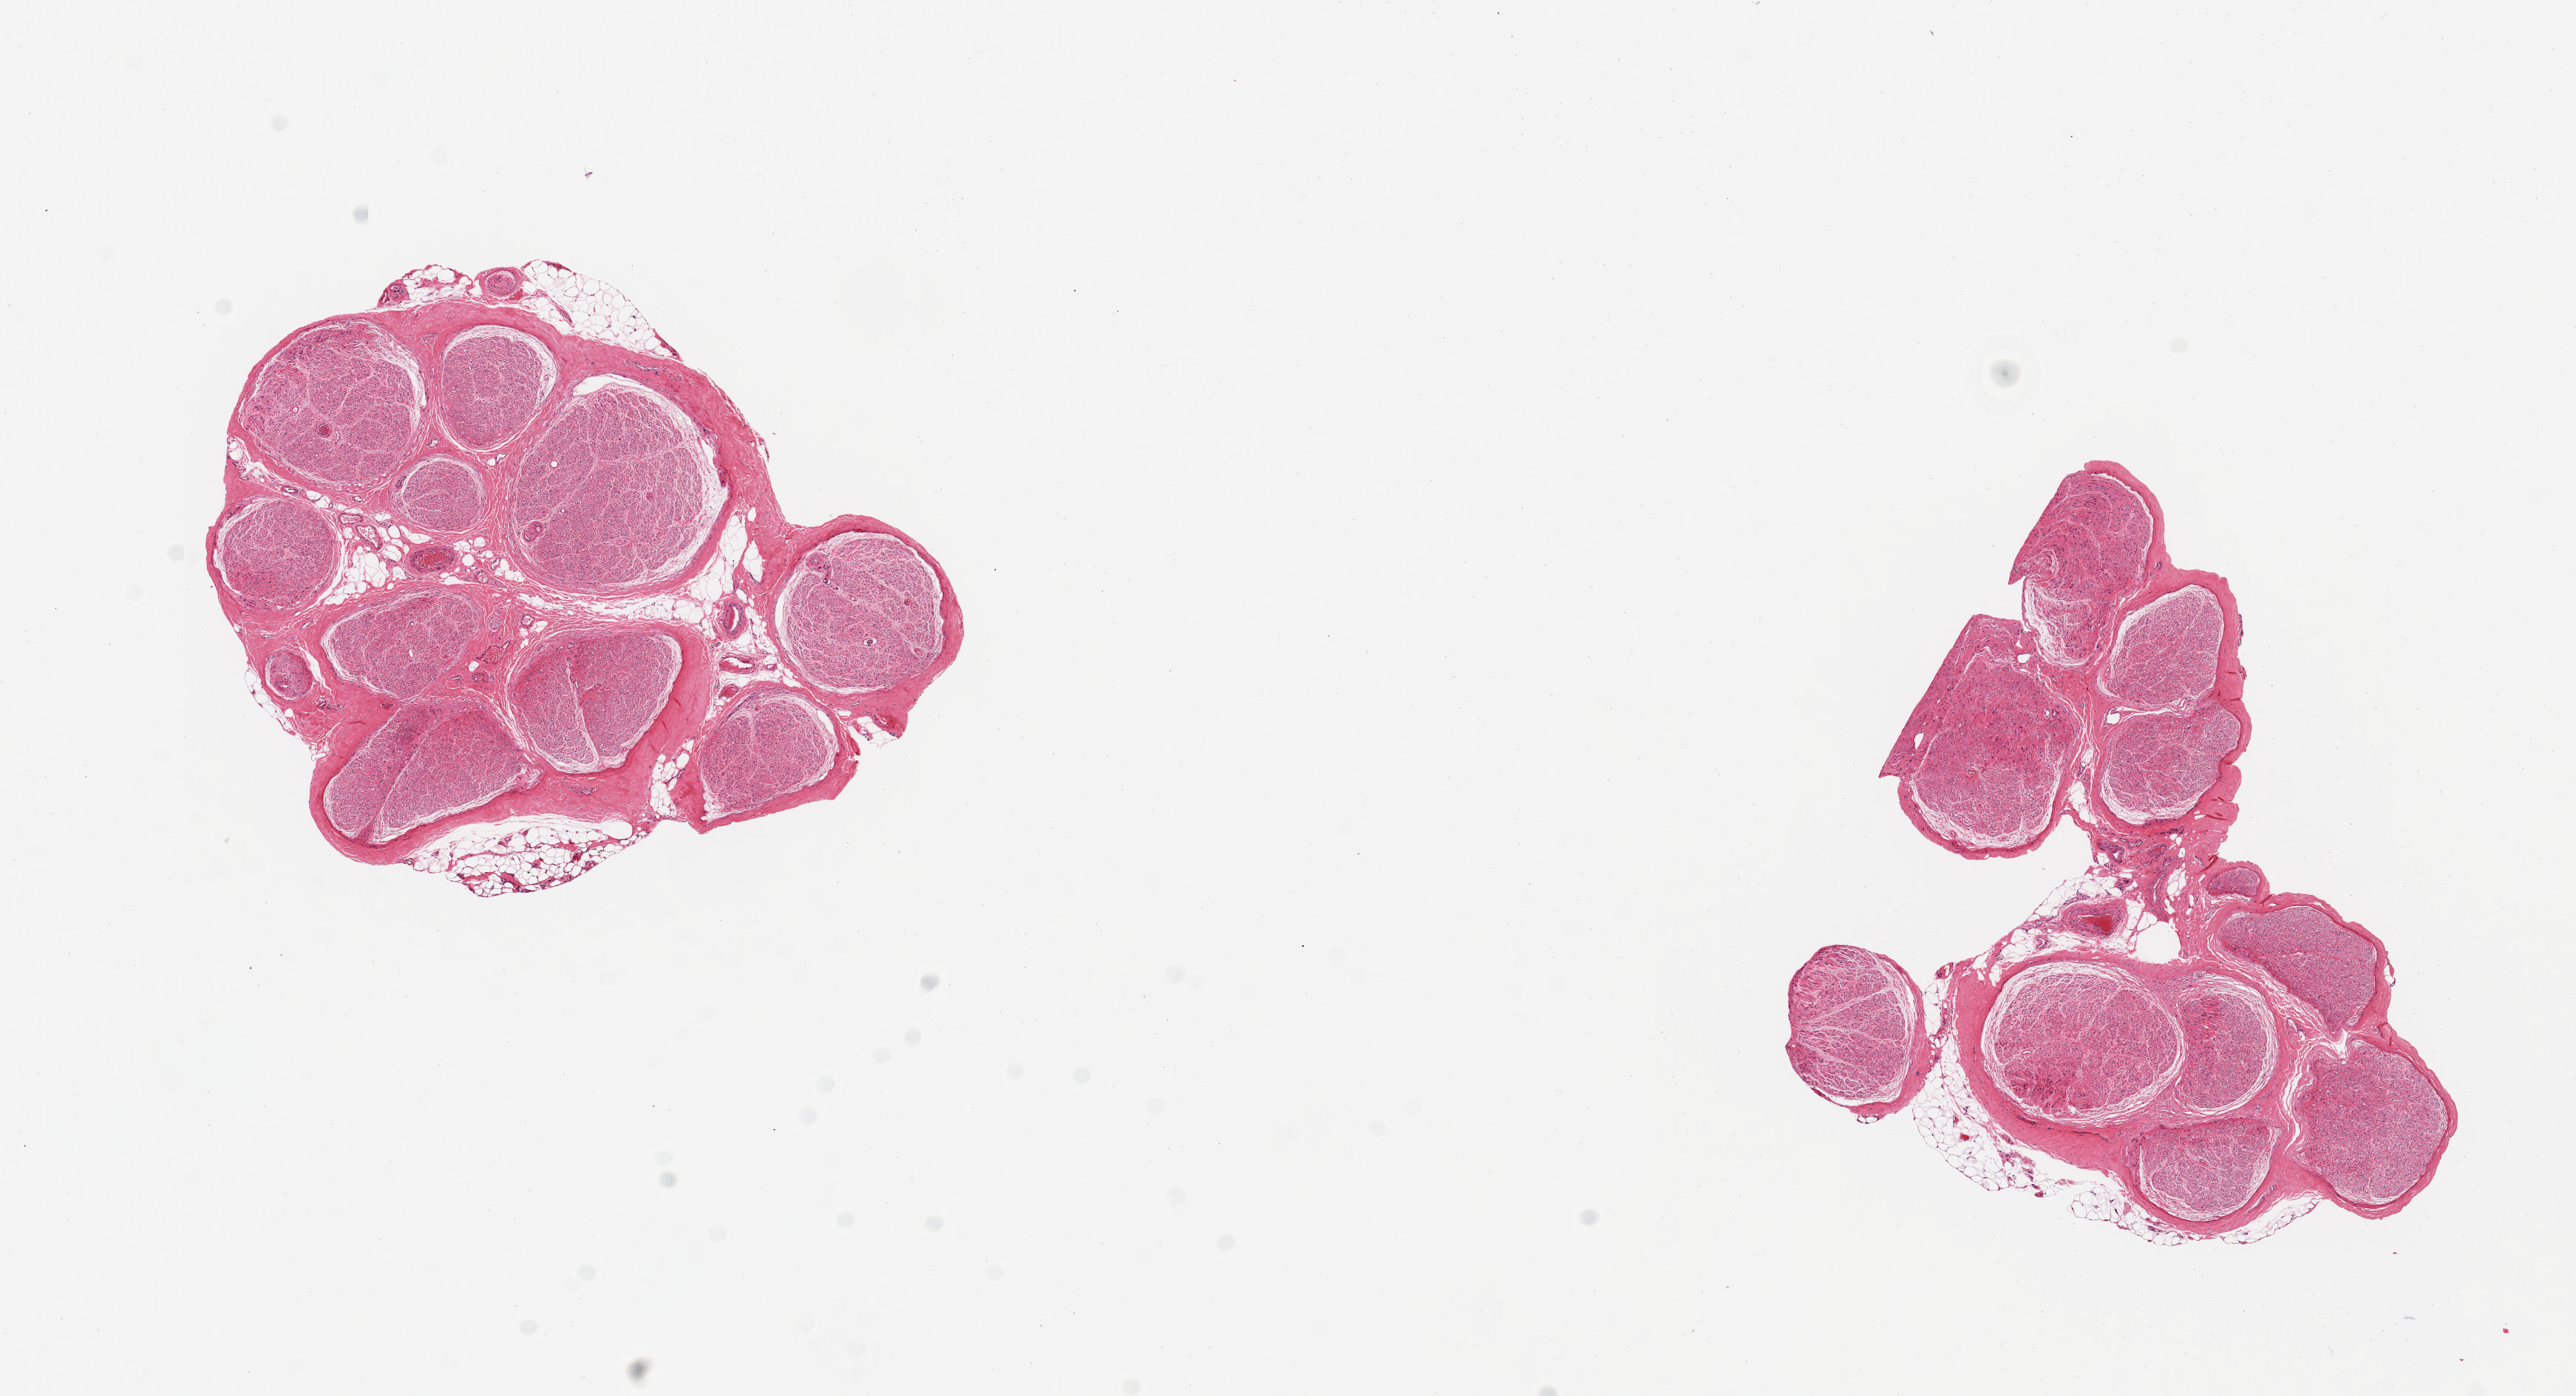
Whole-slide image, haematoxylin and eosin stain, brightfield, shown as a low-resolution overview of the whole scanned area (about 13.8 x 7.5 mm, acquisition: 20x scan); PAXgene-fixed, paraffin-embedded tissue; target tissue: tibial nerve; donor tissue sample. Donor sex: male.
Pathologist's review note for this sample: 2 pieces ~4mm d. Reasonably clean specimens, minute amounts of adherent fat, ~0.3mm thick.